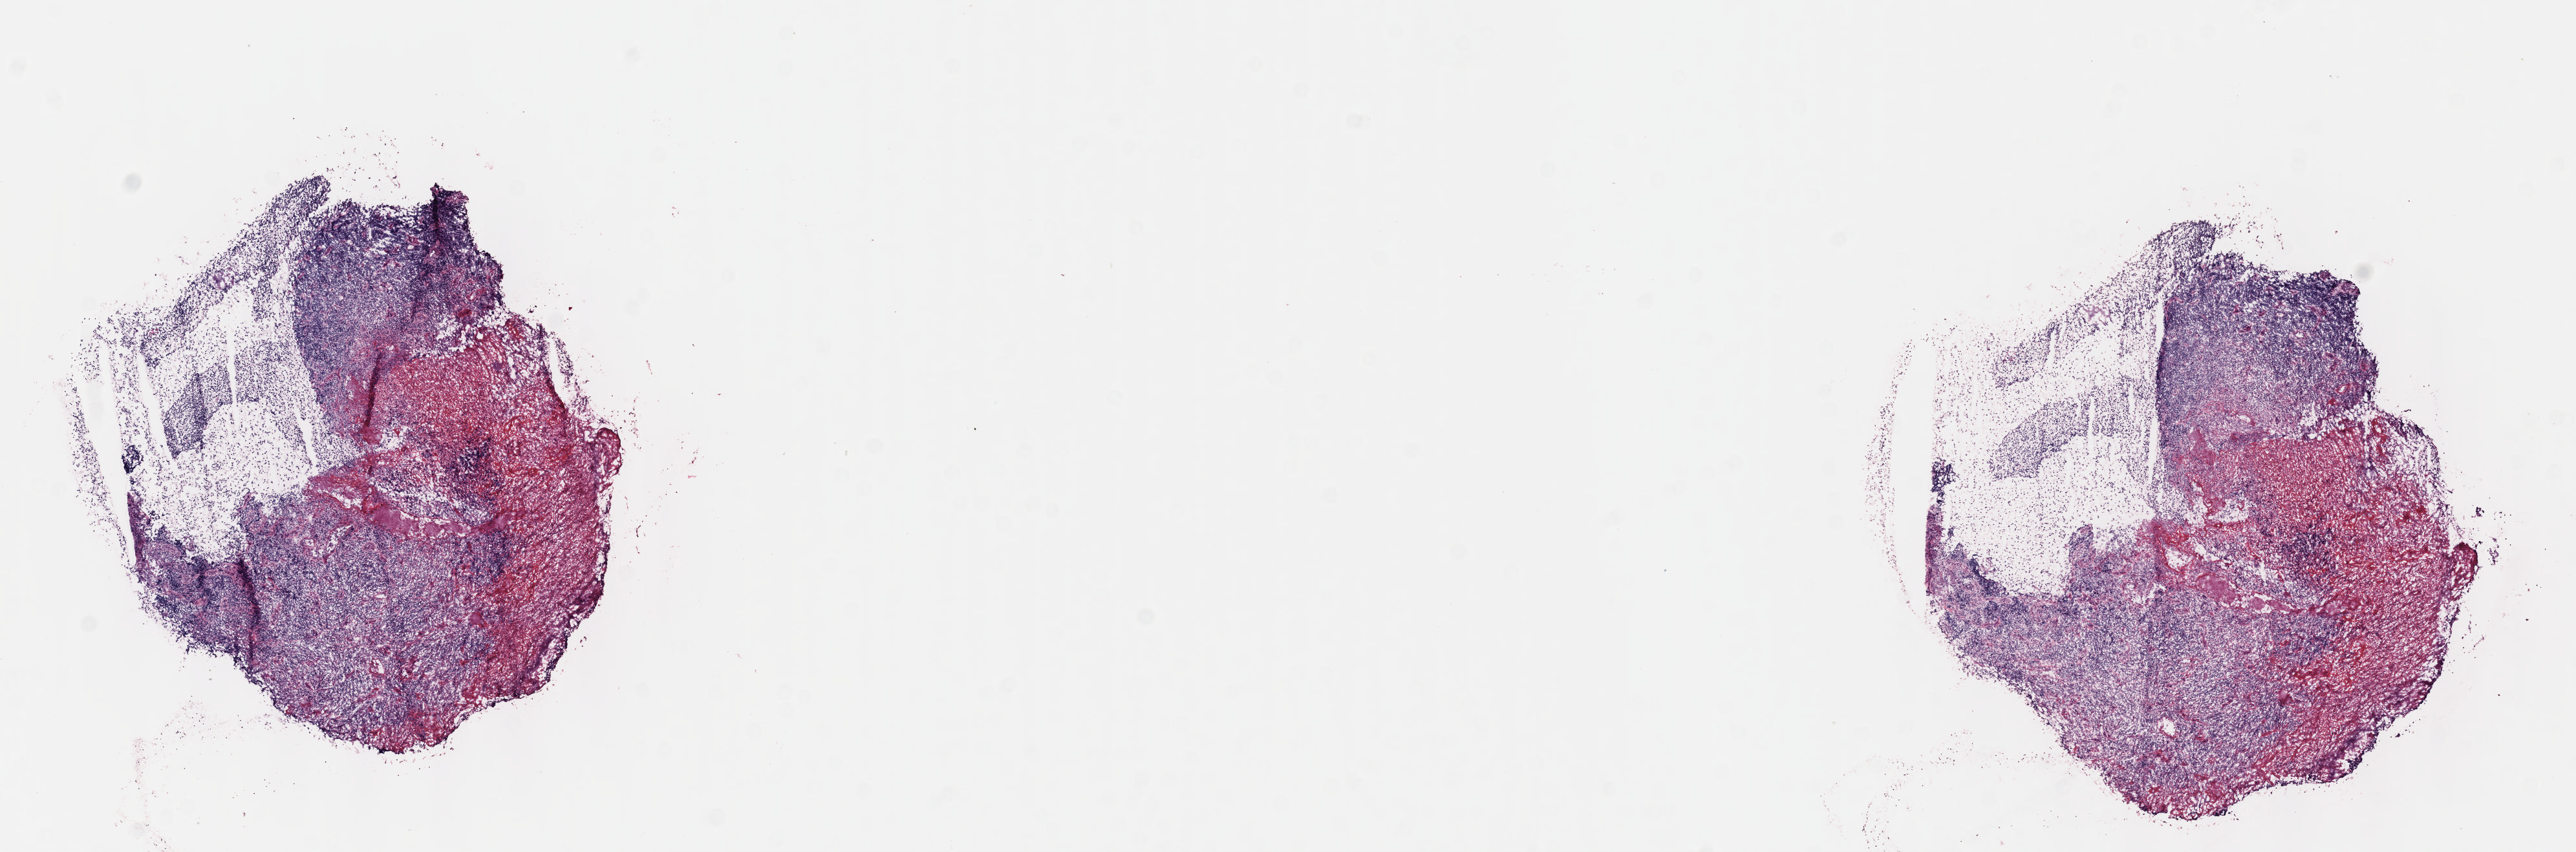
Haematoxylin and eosin whole-slide image, low-resolution overview of the scanned area, about 16.1 x 5.3 mm; frozen section; specimen: primary tumor; site: cranium. Patient male; aged 12. Slide review estimates, as recorded: tumor cells 70%, tumor nuclei 80%, stromal cells 5%, necrosis 25%, normal cells 0%. Infiltration values recorded for this section: lymphocyte infiltration 10%, monocyte infiltration 15%, neutrophil infiltration 15%.
• histologic diagnosis: Burkitt lymphoma, NOS
• Ann Arbor stage (patient): Stage I
• section: top of the tissue portion